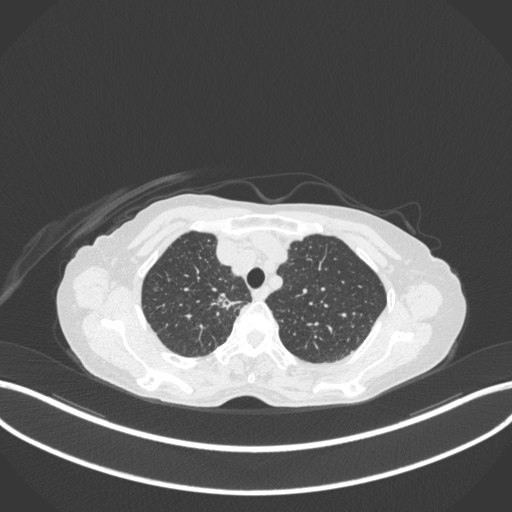
Chest CT, one axial slice. Position 303 of 363 along the scan axis. 120 kVp. Lung window (W 1500 / L -600 HU). 1 mm slice thickness. 512 × 512 image matrix, field of view 400 × 400 mm. Female patient, age 75 years. Case-level facts recorded for this patient, not image findings: clinical TNM (as recorded): T1c N1 M1.
Outlined on this slice (bounding box drawn by a radiologist):
- lung tumour (recorded histology: adenocarcinoma): bounding box [x1, y1, x2, y2] px = [212, 288, 242, 313]